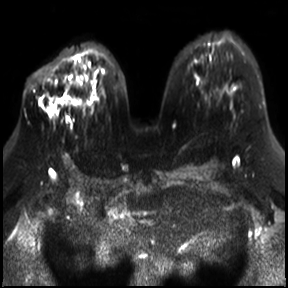
Breast MRI, one axial slice. Slice 17 of 30 in the series (ordered by position). Diffusion-weighted series; image 2 of 4 stored at this slice position (different b-values; order by instance number). 3 T. 288 × 288 image matrix, field of view 340 × 340 mm. Female patient.
Annotated regions visible in this slice (expert manual segmentation):
- tumour on diffusion-weighted imaging: bounding box <48,100,63,115> (left, top, right, bottom; pixels)